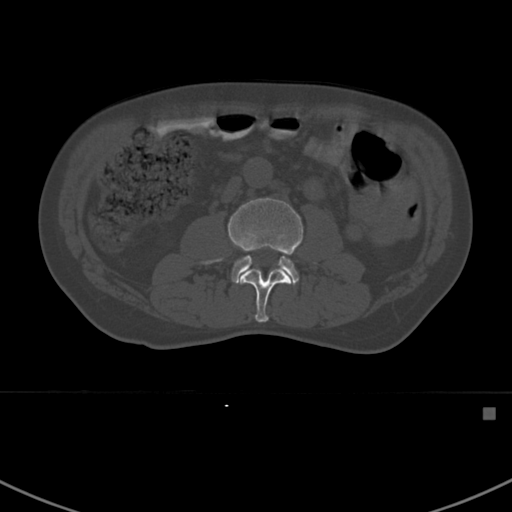
CT including the spine, one axial slice. Slice 274 of 412 in the series (ordered by position). 120 kVp. Bone window (W 1800 / L 400 HU). 1.5 mm slice thickness. 512 × 512 image matrix, field of view 358 × 358 mm. Male patient, age 59 years. From the clinical record (not read from this slice): primary cancer: prostate.
Outlined on this slice (semi-automatic segmentation, software-assisted and operator-edited):
- L2 vertebra: bounding box (x1, y1, x2, y2) in pixels: (240, 268, 292, 323)
- L3 vertebra: (200, 197, 304, 284)